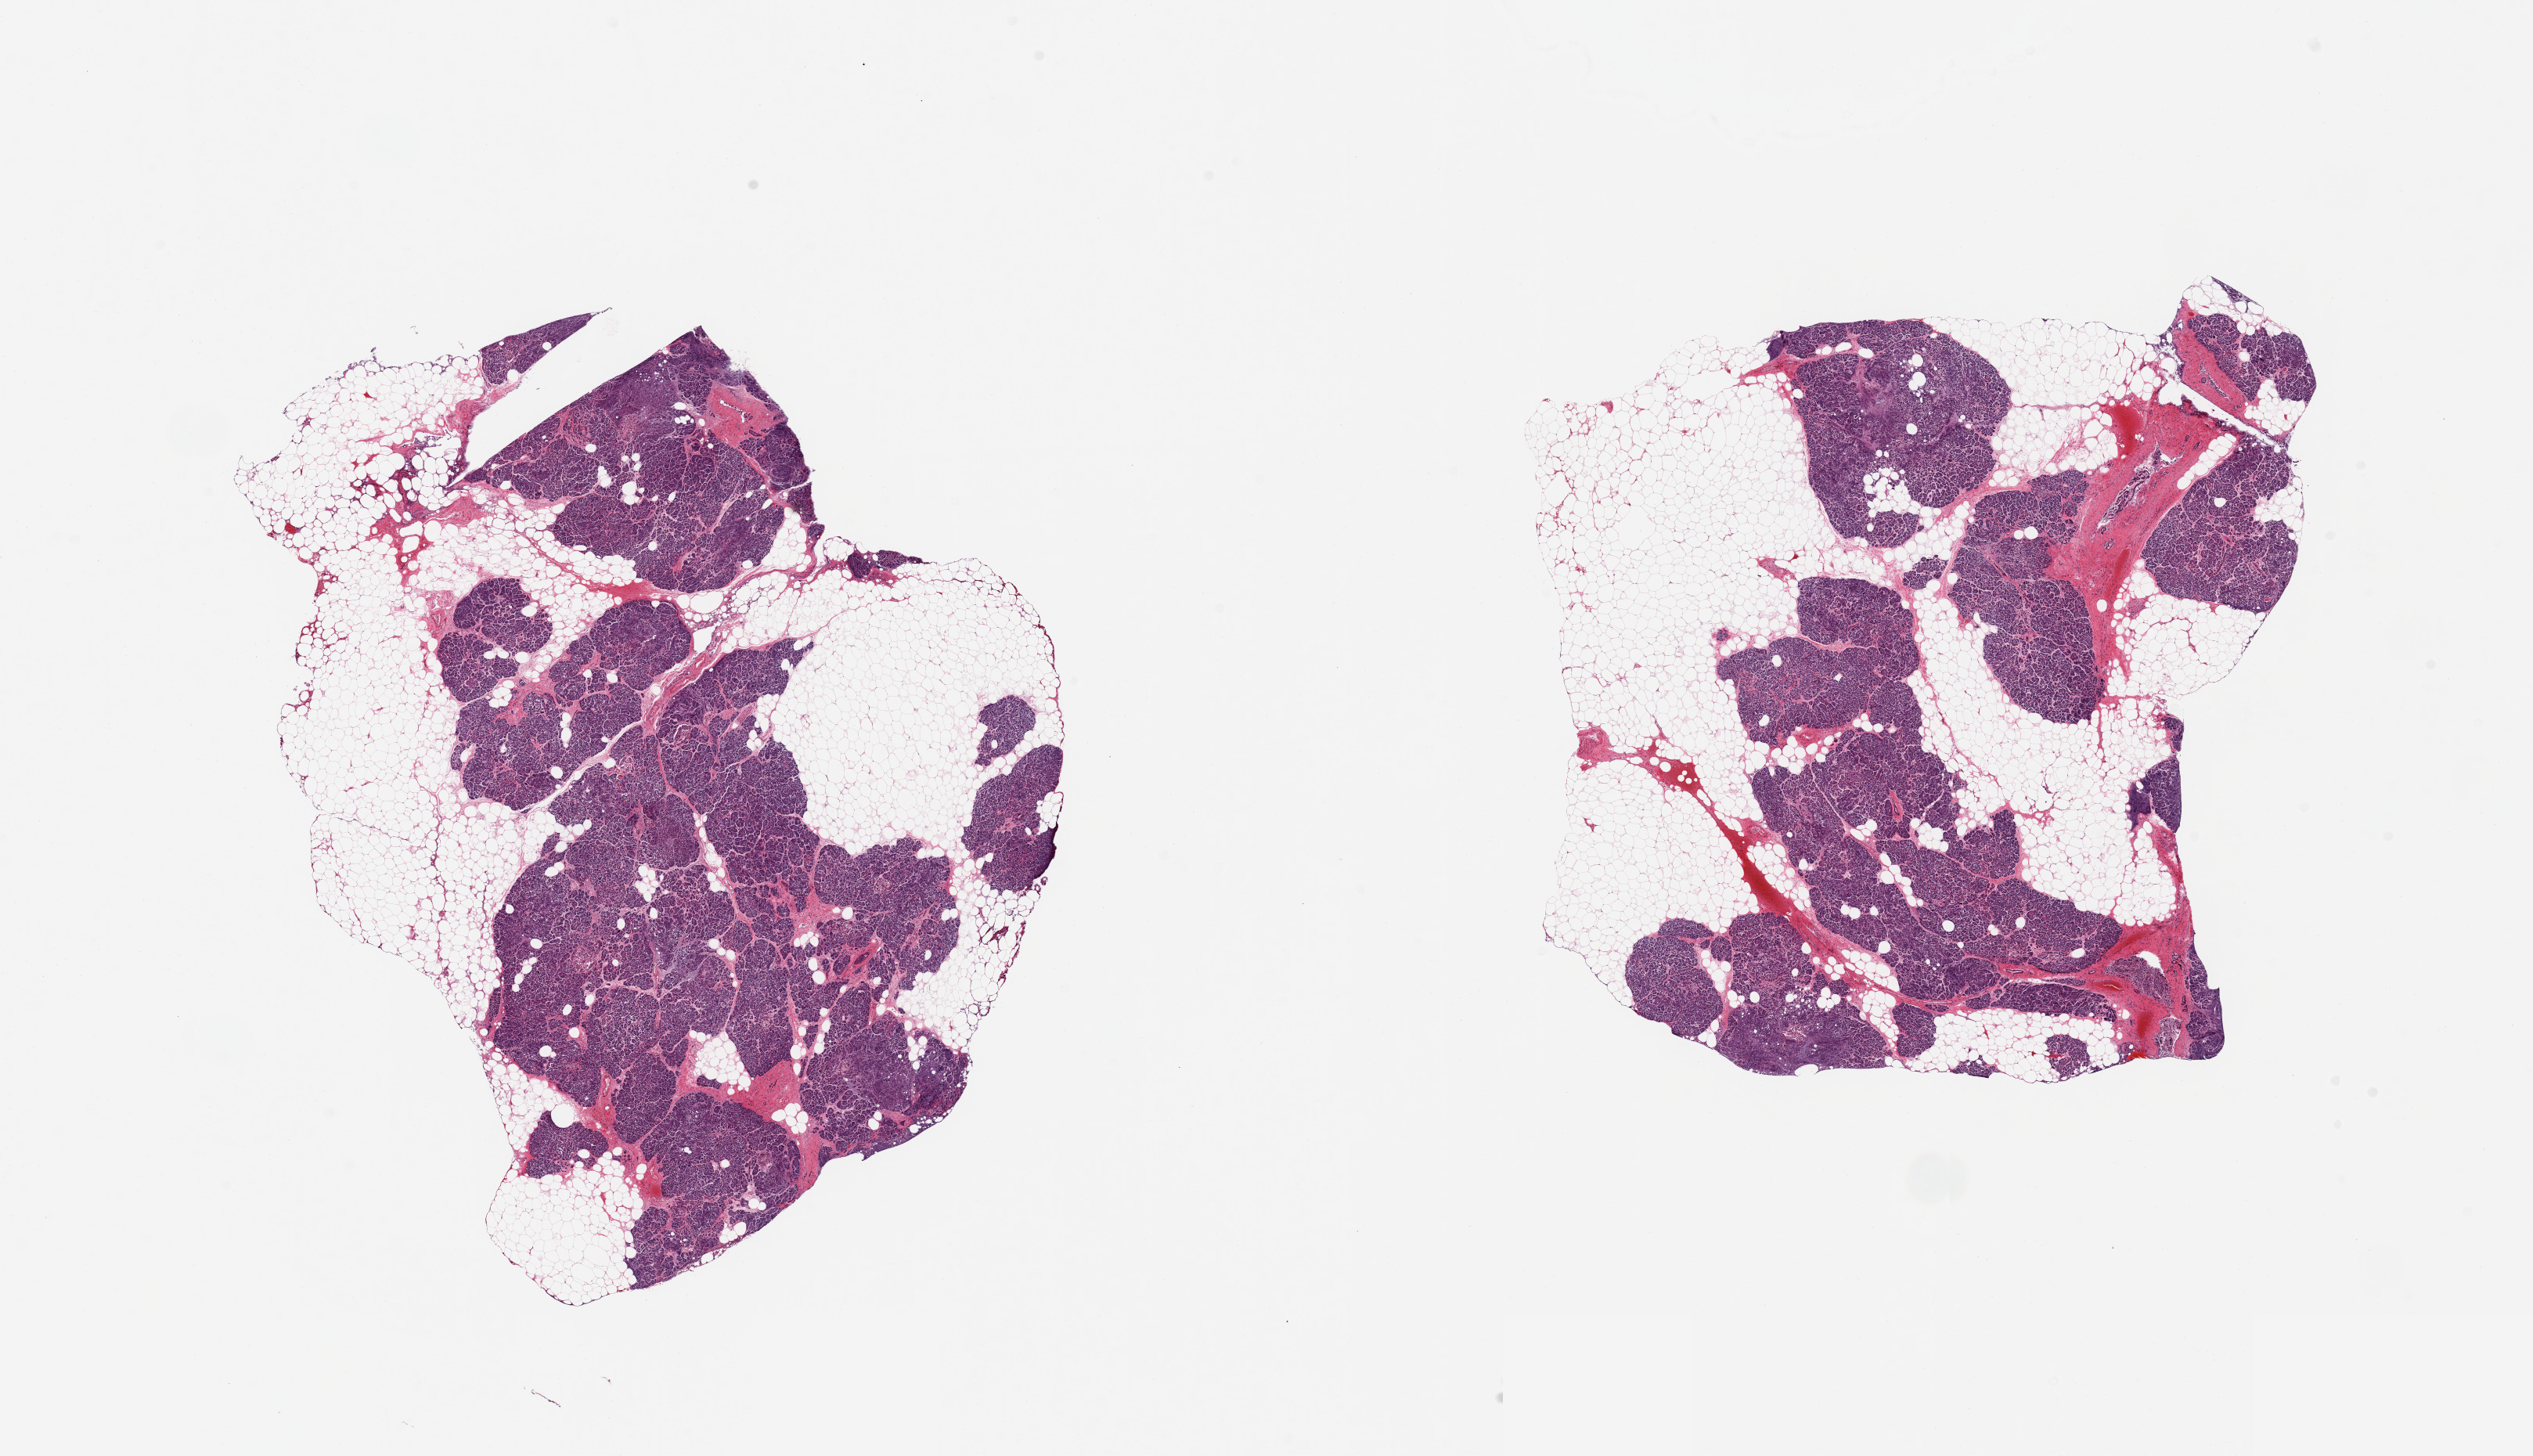
Digitized haematoxylin and eosin-stained section, a low-resolution overview of the entire scanned area, about 25.6 x 14.7 mm, PAXgene-fixed paraffin-embedded (PFPE) section, sampled site (target tissue): pancreas, tissue donor sample. Male donor.
Review note (as recorded): 2 pieces; 40% internal & external fat.